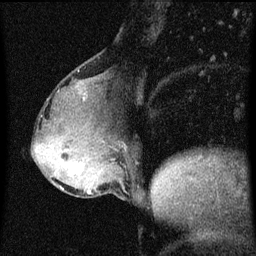
Breast MRI (dynamic contrast-enhanced), one sagittal slice. Position 26 of 60 along the scan axis. Dynamic contrast-enhanced series, image 2 of 3 at this slice position (ordered by acquisition). 1.5 T. TE 4.2 ms, TR 8 ms. 256 × 256 image matrix, field of view 180 × 180 mm. Female patient, age 49 years.
Structures marked on this image (semi-automatically segmented with operator editing):
- analysis volume of interest (the breast-tissue region the enhancement analysis was run in; not a lesion): bounding box [x1, y1, x2, y2] px = [51, 158, 96, 185]
- tumour enhancement mask (voxels above the 70 % enhancement threshold inside the analysis volume of interest): [72, 162, 84, 175]